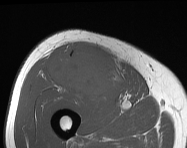
MRI of an extremity soft-tissue mass, one axial slice. Position 75 of 114 along the scan axis. MR volume resampled by the dataset authors to the PET/CT grid (not the native acquisition matrix). 3.27 mm slice thickness. 187 × 148 image matrix. Male patient. From the clinical record (not read from this slice): histological type: pleiomorphic leiomyosarcoma; grade: intermediate; site of the primary tumour: right thigh.
Structures marked on this image (expert contour drawn on MRI and transferred to this co-registered scan by the dataset authors):
- gross tumour volume including surrounding oedema: bounding box <50,45,117,98> (left, top, right, bottom; pixels)
- gross tumour volume (mass): <50,47,117,98>